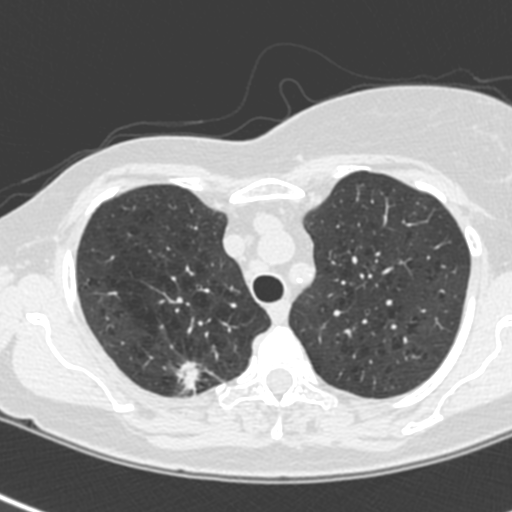
Low-dose screening chest CT, one axial slice; slice 175 of 214 in the series (ordered by position); 120 kVp; lung window (W 1500 / L -600 HU); 512 × 512 image matrix, field of view 281 × 281 mm.
Outlined on this slice (outlined manually by an expert reader):
- lesion 1 (tumor, upper lobe of right lung): bounding box (x1, y1, x2, y2) in pixels: (177, 361, 201, 393)